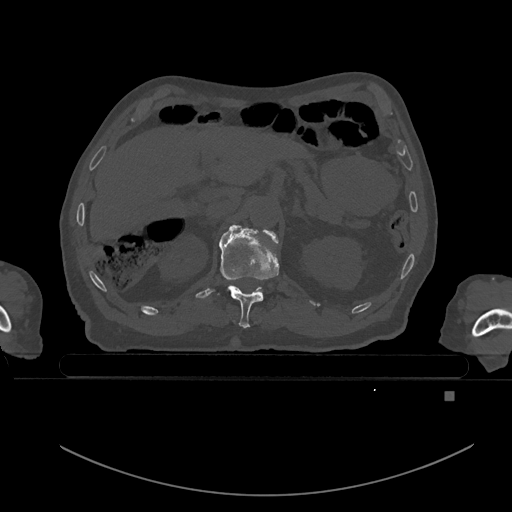
CT including the spine, one axial slice; position 11 of 969 along the scan axis; bone window (W 1800 / L 400 HU); 512 × 512 image matrix, field of view 456 × 456 mm. Male patient, age 82 years. From the clinical record (not read from this slice): primary cancer: prostate; vertebrae with lytic lesions (as recorded): T11, T9, T8, T2.
Annotated regions visible in this slice (semi-automatically segmented with operator editing):
- T11 vertebra: box from (x=217, y=227) to (x=279, y=328) px